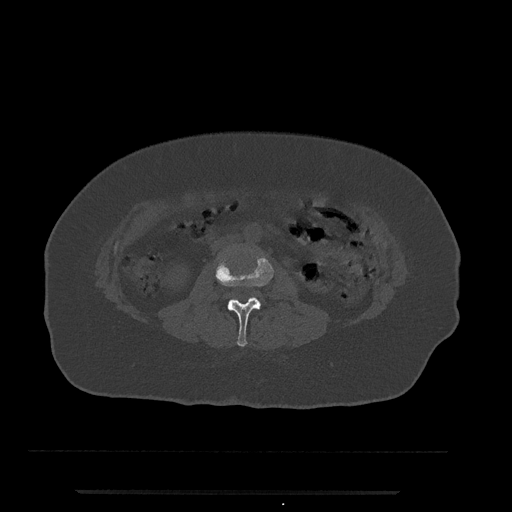
CT including the spine, one axial slice; position 15 of 797 along the scan axis; reconstruction kernel Br40s/3; 120 kVp; bone window (W 1800 / L 400 HU); 0.5 mm slice thickness; 512 × 512 image matrix. Female patient, age 51 years. Case-level facts recorded for this patient, not image findings: primary cancer: neuro; vertebrae with lytic lesions (as recorded): T8.
Annotated regions visible in this slice (semi-automatically segmented with operator editing):
- L2 vertebra: box from (x=215, y=250) to (x=274, y=347) px